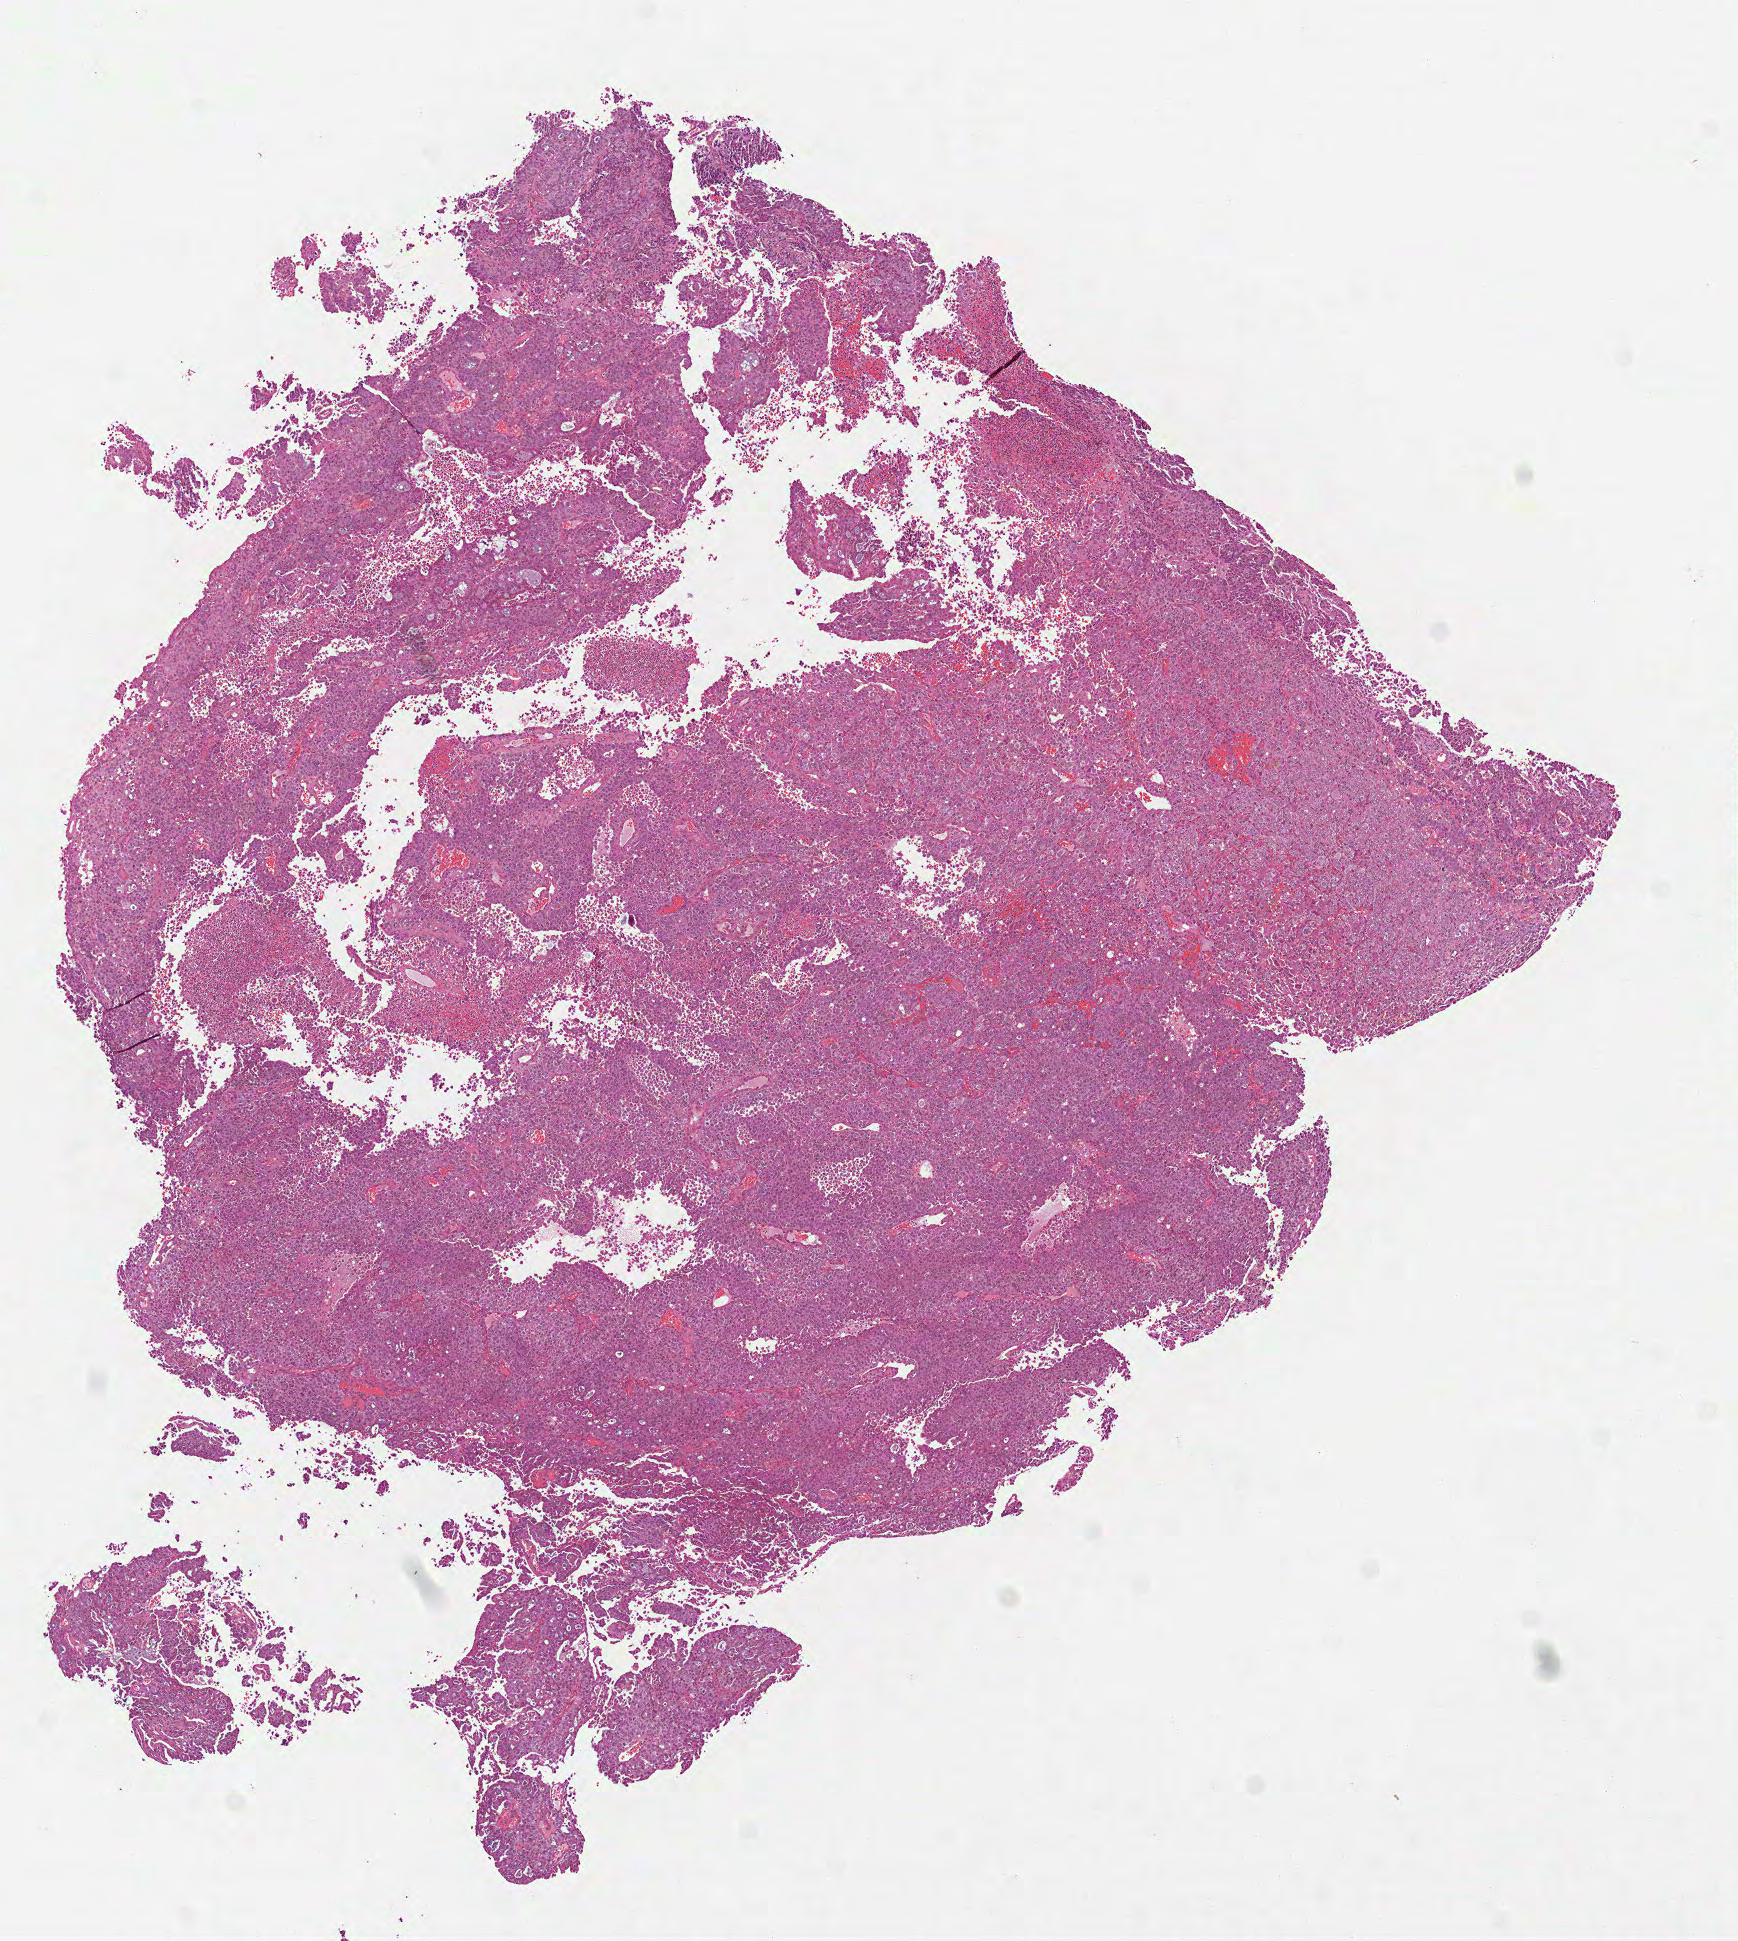
Digitized H&E-stained tissue section (whole slide), low-resolution overview of the scanned area, about 7.0 x 7.8 mm (slide scanned at 40x). FFPE section. Uterus, primary tumour sample. Female, age 53 years at initial diagnosis. Histologic grade: G3 (poorly differentiated).
FIGO stage: IVB. Histologic diagnosis: Serous cystadenocarcinoma, NOS.